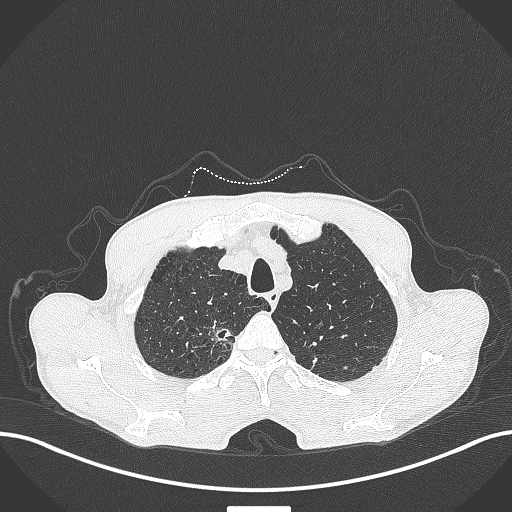
Chest CT, one axial slice; position 364 of 445 along the scan axis; lung window (W 1500 / L -600 HU); 1 mm slice thickness; 512 × 512 image matrix, field of view 400 × 400 mm. Male patient, age 70 years. Case-level facts recorded for this patient, not image findings: clinical TNM (as recorded): T1a N0 M0; histopathological grade: G1-2.
Structures marked on this image (rectangle marked by the reading radiologist):
- lung tumour (recorded histology: adenocarcinoma): box from (x=209, y=320) to (x=238, y=342) px